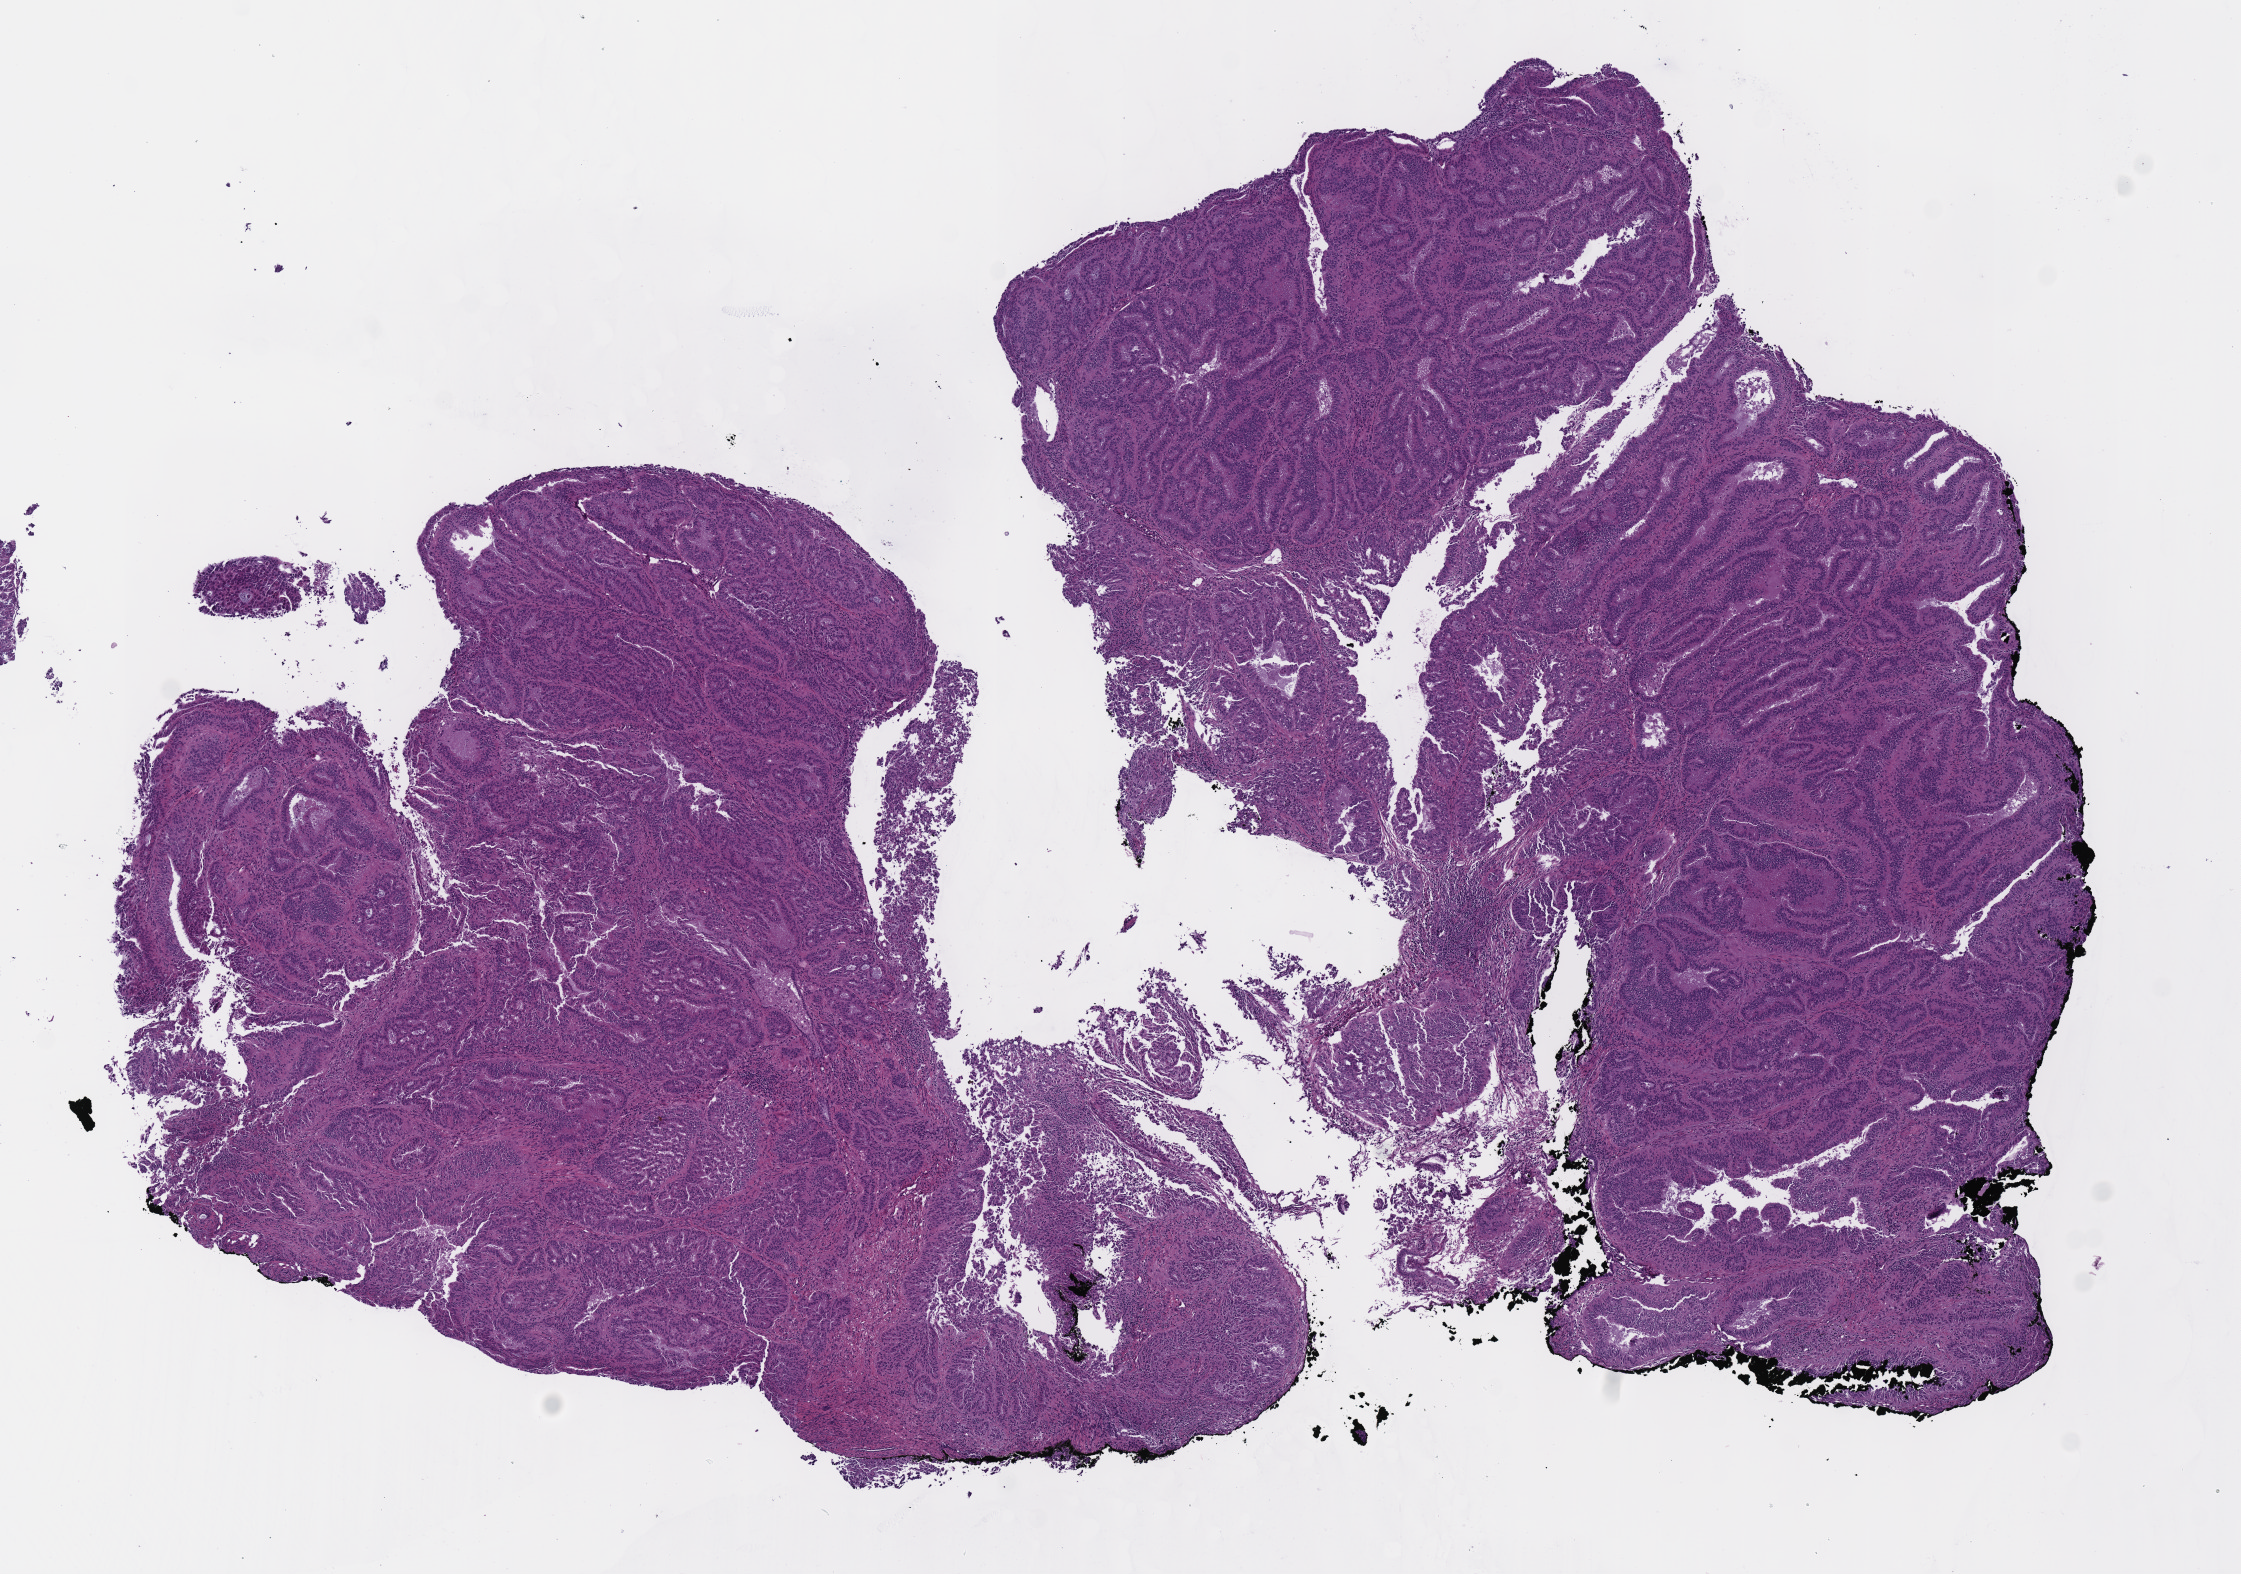
Whole-slide histology image, H&E-stained, shown as a low-resolution overview of the whole scanned area (about 8.8 x 6.2 mm, from a 40x scan), FFPE section, primary tumour sample from the uterus. Female patient; age at initial diagnosis 73 years. Histologic grade: G3 (poorly differentiated).
Lymph nodes positive (case pathology): 0 of 21 examined. Diagnosis: Serous cystadenocarcinoma, NOS (endometrium). FIGO stage: IA.